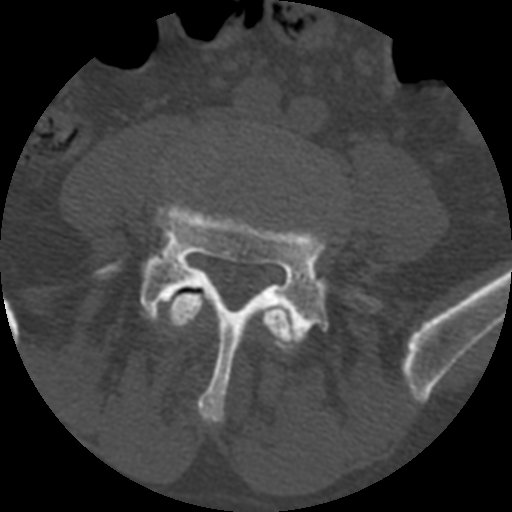
CT including the spine, one axial slice. Position 264 of 399 along the scan axis. Reconstruction kernel STANDARD. 120 kVp. Bone window (W 1800 / L 400 HU). 1.25 mm slice thickness. 512 × 512 image matrix, field of view 160 × 160 mm. Patient age 71 years. From the clinical record (not read from this slice): primary cancer: prostate.
Structures marked on this image (semi-automatically segmented with operator editing):
- L4 vertebra: bounding box <166,292,296,348> (left, top, right, bottom; pixels)
- L5 vertebra: <98,202,381,424>